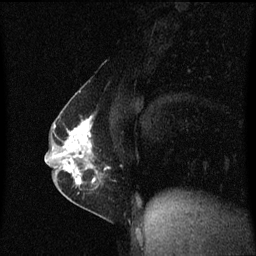
Breast MRI (dynamic contrast-enhanced), one sagittal slice; position 30 of 60 along the scan axis; dynamic contrast-enhanced series, image 2 of 3 at this slice position (ordered by acquisition); 1.5 T; TE 4.2 ms, TR 8.4 ms; 2 mm slice thickness; 256 × 256 image matrix. Female patient, age 40 years.
Structures marked on this image (semi-automatic segmentation, software-assisted and operator-edited):
- analysis volume of interest (the breast-tissue region the enhancement analysis was run in; not a lesion): bounding box [x1, y1, x2, y2] px = [57, 110, 108, 191]
- tumour enhancement mask (voxels above the 70 % enhancement threshold inside the analysis volume of interest): [63, 116, 108, 187]